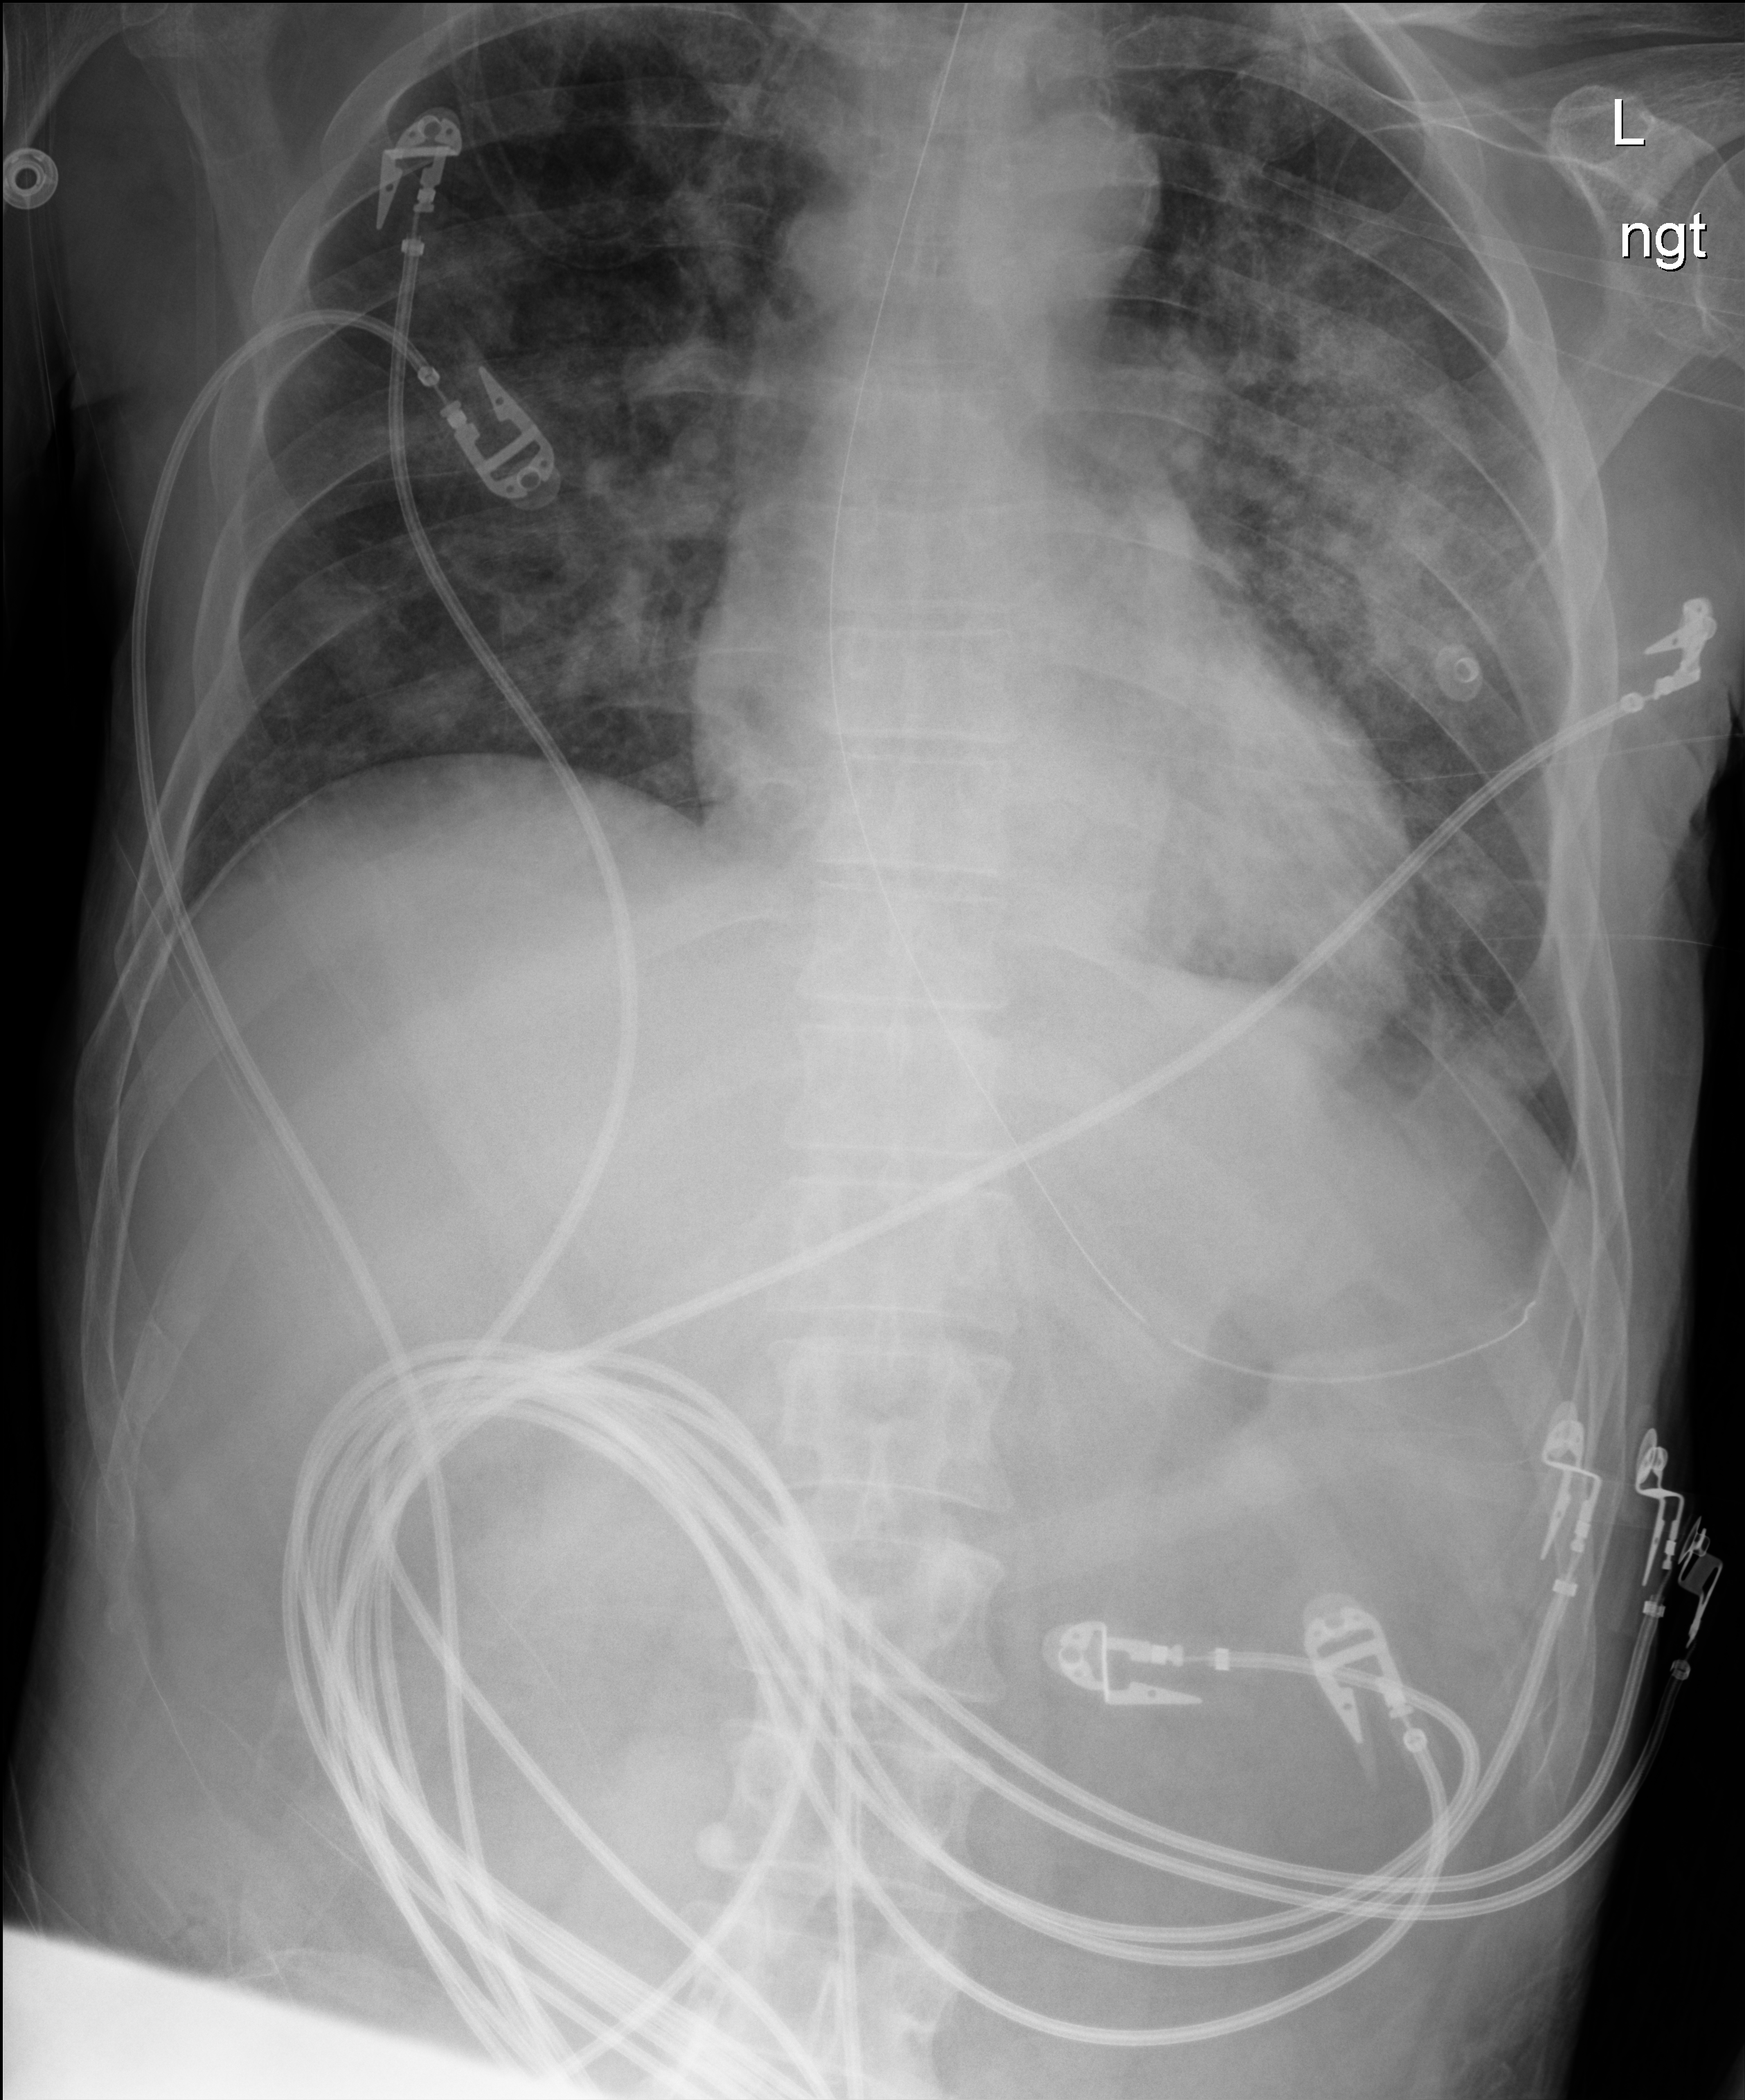
Chest X-ray (portable), anteroposterior (AP) projection. Patient hospitalised with COVID-19; male, aged 18–59 years.
Admission-level facts for this patient (not findings on this image; timing relative to this image not recorded):
- admitted to intensive care during this hospital stay: yes